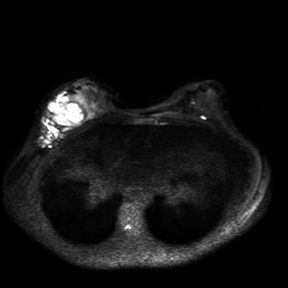
Breast MRI, one axial slice. Slice 20 of 30 in the series (ordered by position). Diffusion-weighted series; image 2 of 4 stored at this slice position (different b-values; order by instance number). 3 T. 288 × 288 image matrix, field of view 360 × 360 mm. Female patient.
Structures marked on this image (manually delineated by an expert):
- tumour on diffusion-weighted imaging: bounding box [x1, y1, x2, y2] px = [51, 97, 70, 123]